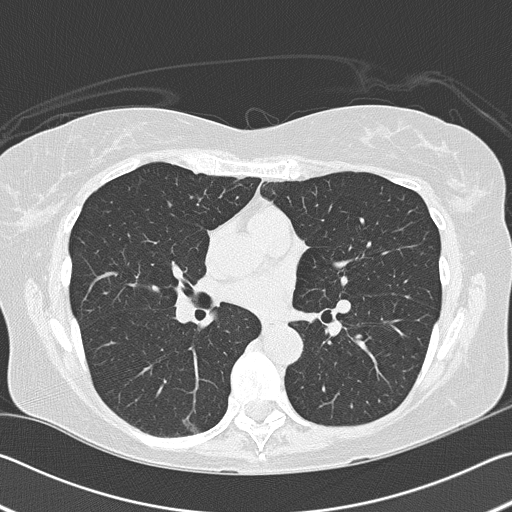
Axial slice from a low-dose chest CT screening exam; first (baseline) screen; lung window (W 1500 / L -600 HU); 2 mm slice thickness; 512 × 512 image matrix, field of view 340 × 340 mm. Female participant, aged 60 years at enrolment. Former smoker at enrolment.
- Lesion marked by an expert reader, box from (x=170, y=406) to (x=214, y=441) px.
- The screening reader recorded 2 non-calcified nodules or masses ≥4 mm on this exam (right lower lobe, right middle lobe); which of them this box marks is not recorded.